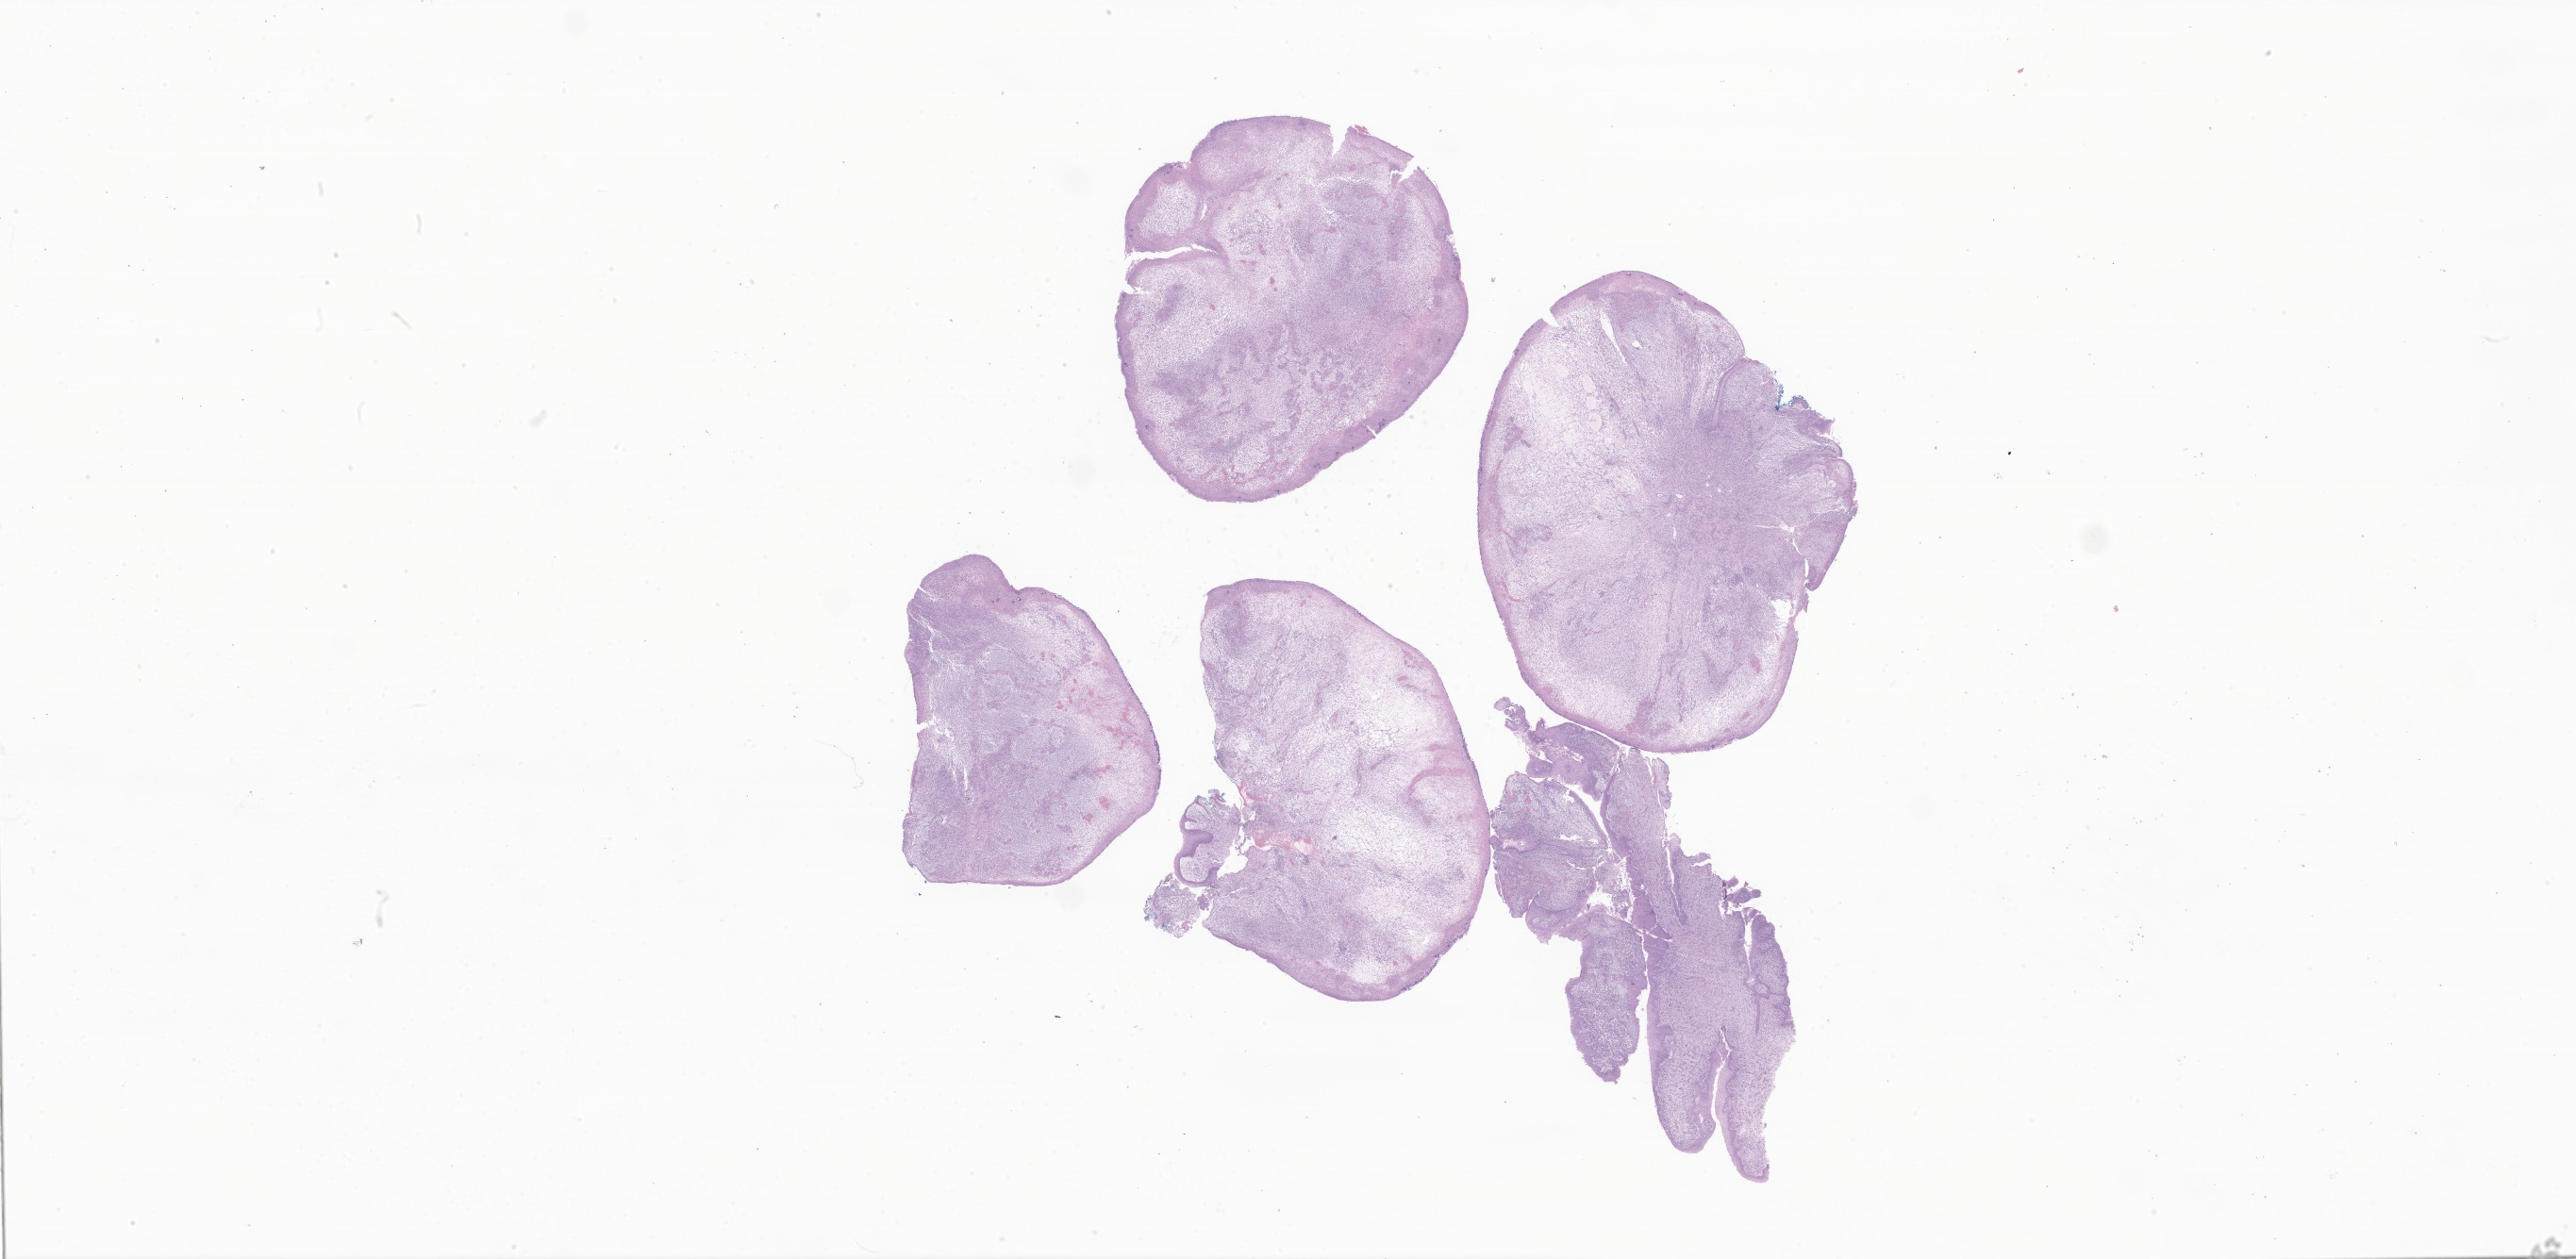
Whole-slide image, hematoxylin and eosin (H&E) stain of tumor tissue from the vagina — whole scanned area (about 46.1 x 22.5 mm) shown as a low-resolution overview. Formalin-fixed paraffin-embedded section. Patient sex: female.
* diagnosis: Embryonal rhabdomyosarcoma, NOS